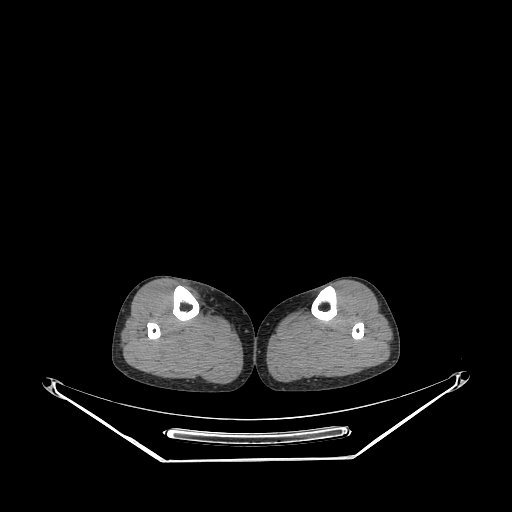
CT of an extremity soft-tissue mass (from a PET/CT study), one axial slice. Position 130 of 267 along the scan axis. Soft-tissue window (W 400 / L 40 HU). 3.75 mm slice thickness. 512 × 512 image matrix, field of view 500 × 500 mm. Female patient. From the clinical record (not read from this slice): histological type: undifferentiated – high grade; grade: high; site of the primary tumour: right thigh.
Structures marked on this image (expert contour drawn on MRI and transferred to this co-registered scan by the dataset authors):
- gross tumour volume (mass): bounding box (x1, y1, x2, y2) in pixels: (187, 288, 199, 300)